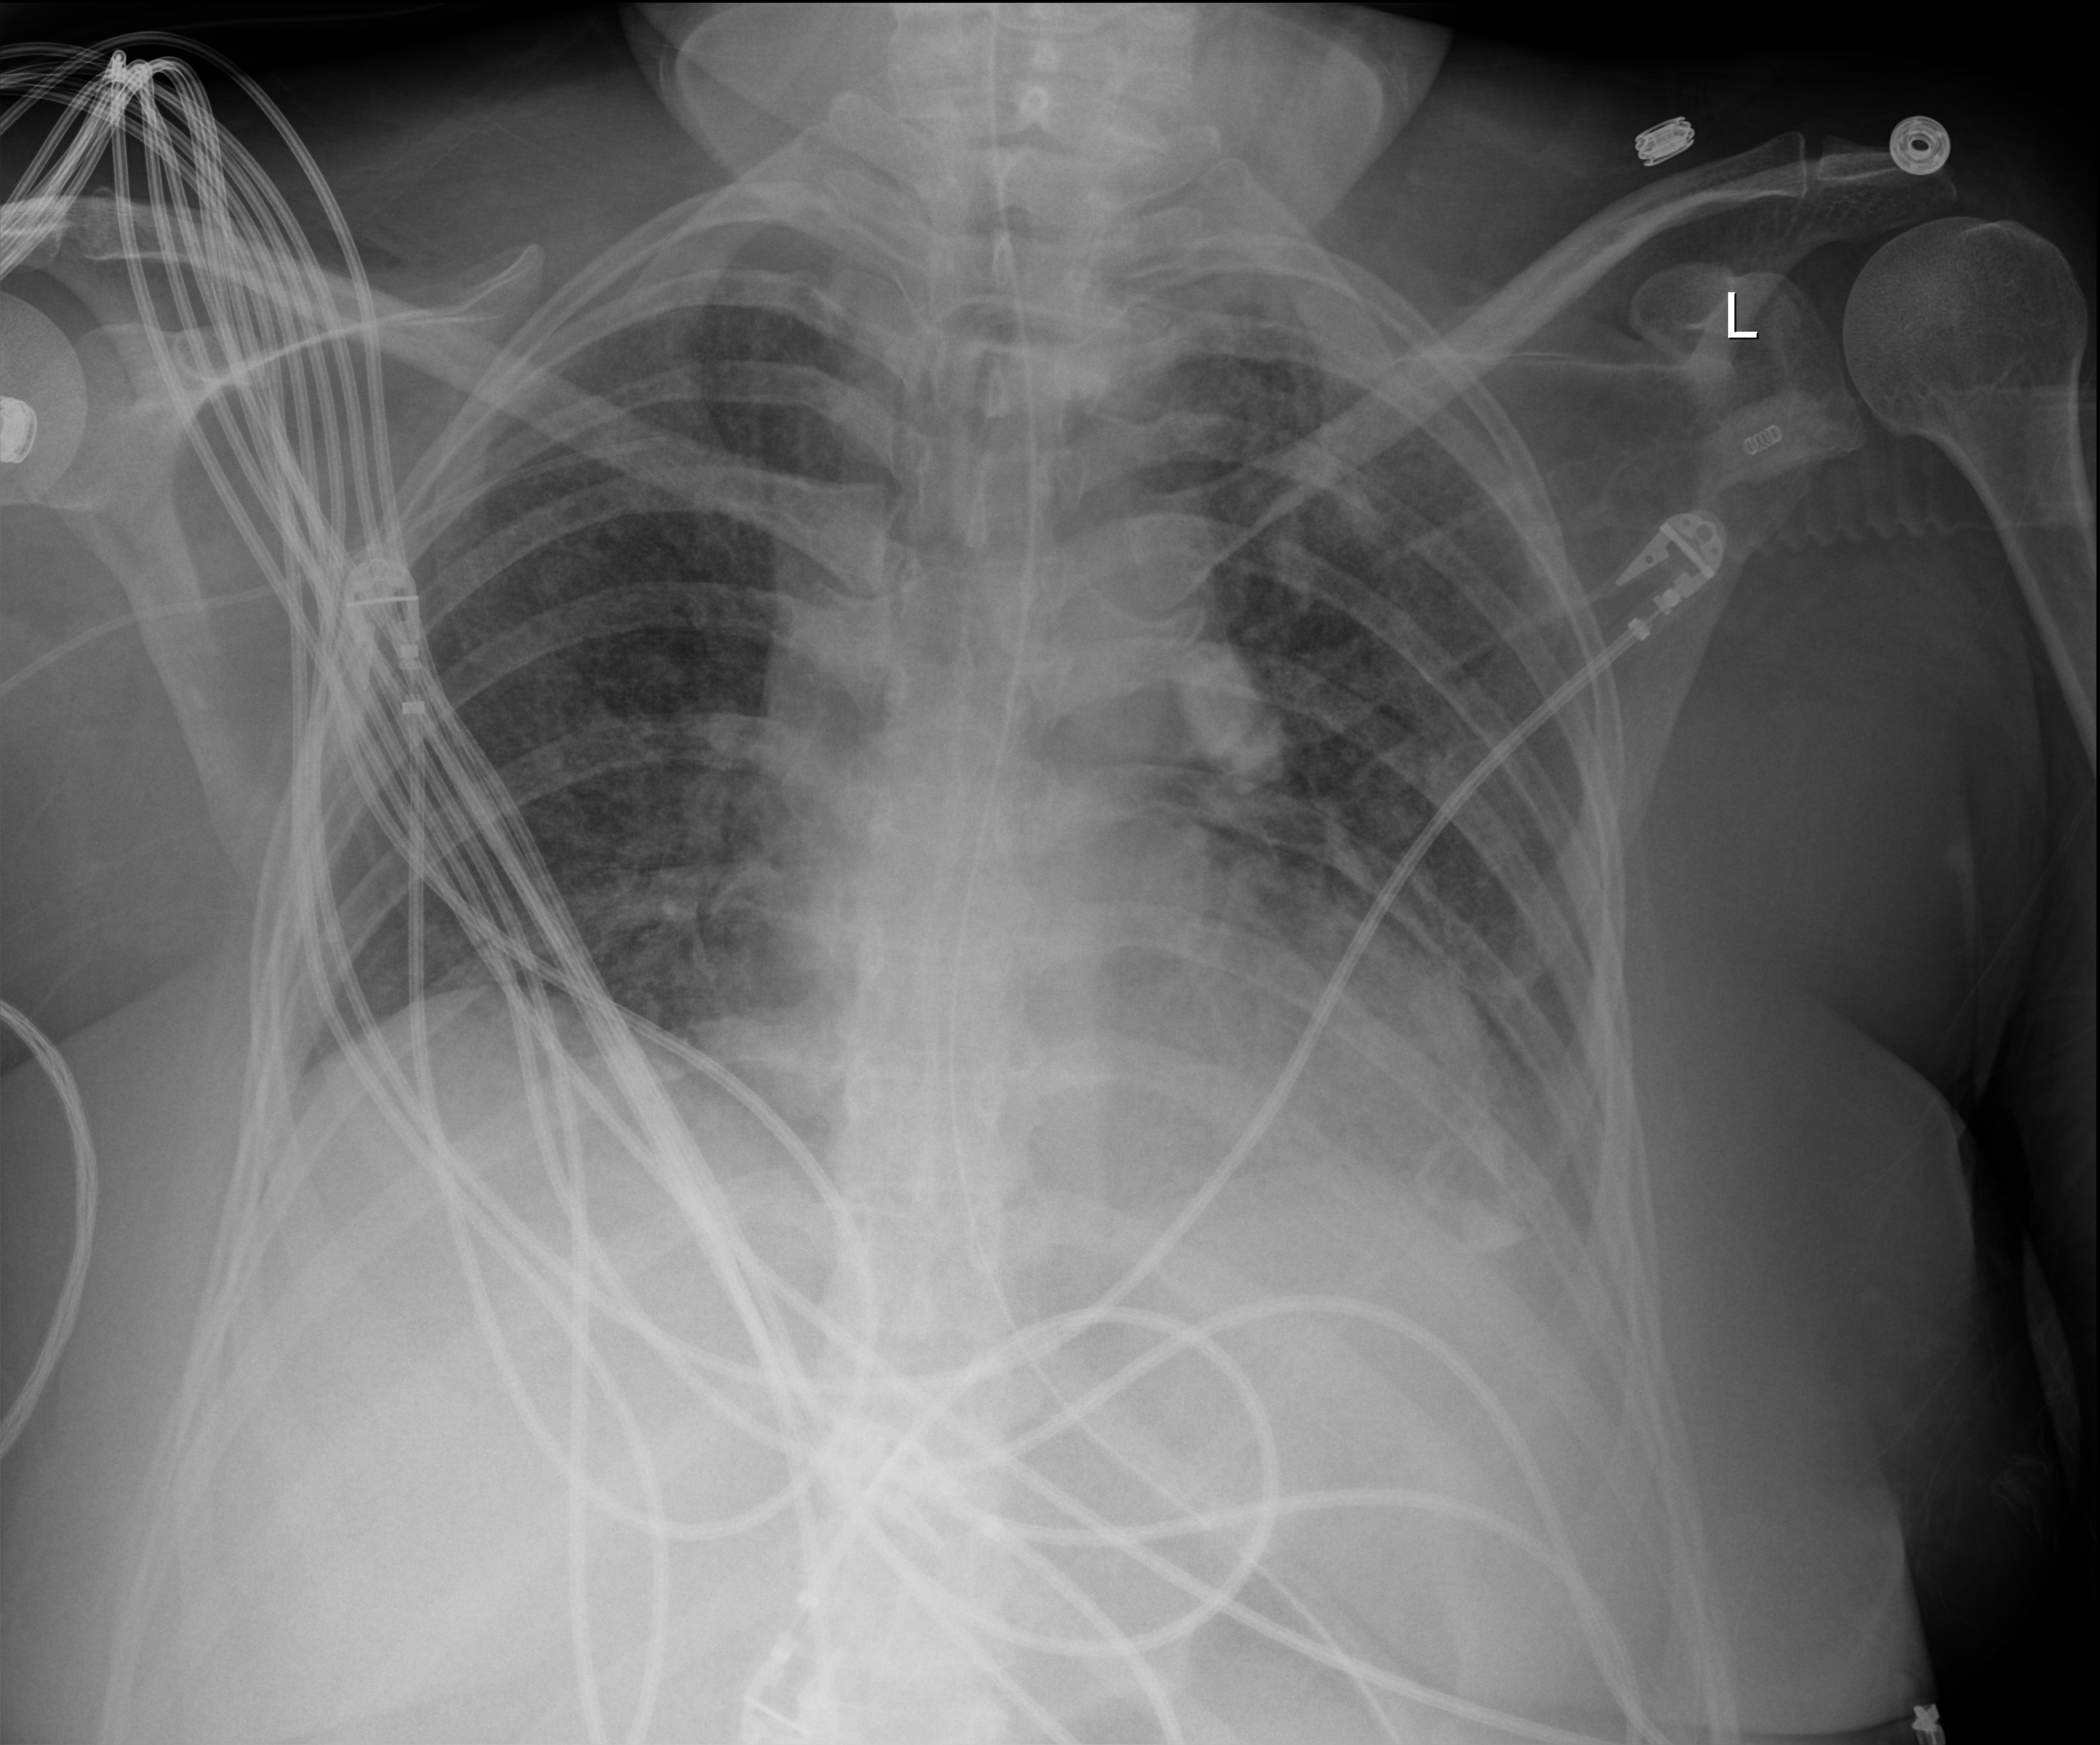
Chest radiograph, anteroposterior (AP) projection. Female patient hospitalised with COVID-19, age 18–59 years.
Admission-level facts for this patient (not findings on this image; timing relative to this image not recorded): hypertension (admission record): no; mechanically ventilated during this hospital stay: yes.